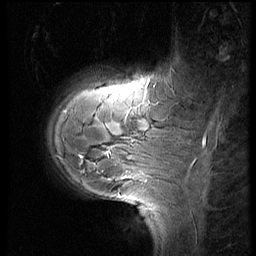
Breast MRI (dynamic contrast-enhanced), one sagittal slice; slice 13 of 60 in the series (ordered by position); 3 images stored at this slice position (order not interpretable as contrast timing); 1.5 T; TE 4.2 ms, TR 8.9 ms; 2.5 mm slice thickness; 256 × 256 image matrix. Female patient, age 29 years. Case-level facts recorded for this patient, not image findings: setting: breast cancer imaged before/during neoadjuvant chemotherapy.
Annotated regions visible in this slice (semi-automatic segmentation, software-assisted and operator-edited):
- analysis volume of interest (the breast-tissue region the enhancement analysis was run in; not a lesion): bounding box (x1, y1, x2, y2) in pixels: (49, 57, 185, 200)
- tumour enhancement mask (voxels above the 140 % enhancement threshold inside the analysis volume of interest): (108, 152, 112, 157)